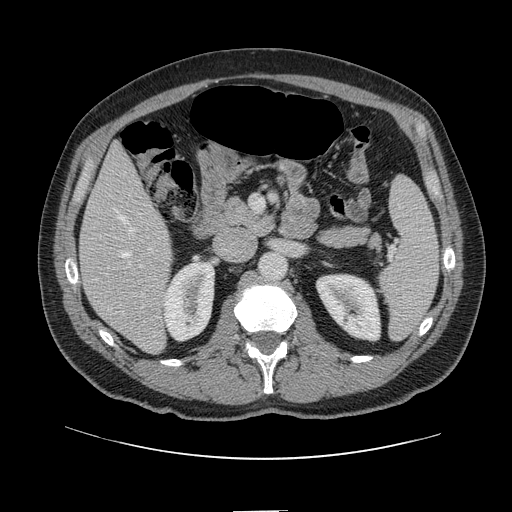
Contrast-enhanced abdominal CT, one axial slice; slice 52 of 161 in the series (ordered by position); soft-tissue window (W 400 / L 40 HU); 2.5 mm slice thickness; 512 × 512 image matrix, field of view 412 × 412 mm. Male patient, age 66 years. From the clinical record (not read from this slice): diagnosis: colorectal cancer liver metastases, imaged before liver resection; multiple liver metastases: no; largest metastasis: 3.5 cm; disease in both lobes: no.
Annotated regions visible in this slice (manually delineated by an expert):
- hepatic veins: bounding box <118,213,134,258> (left, top, right, bottom; pixels)
- liver: <81,146,172,353>
- planned liver remnant (the part of the liver to remain after resection): <81,147,163,277>
- portal vein (with intrahepatic branches): <127,246,157,297>